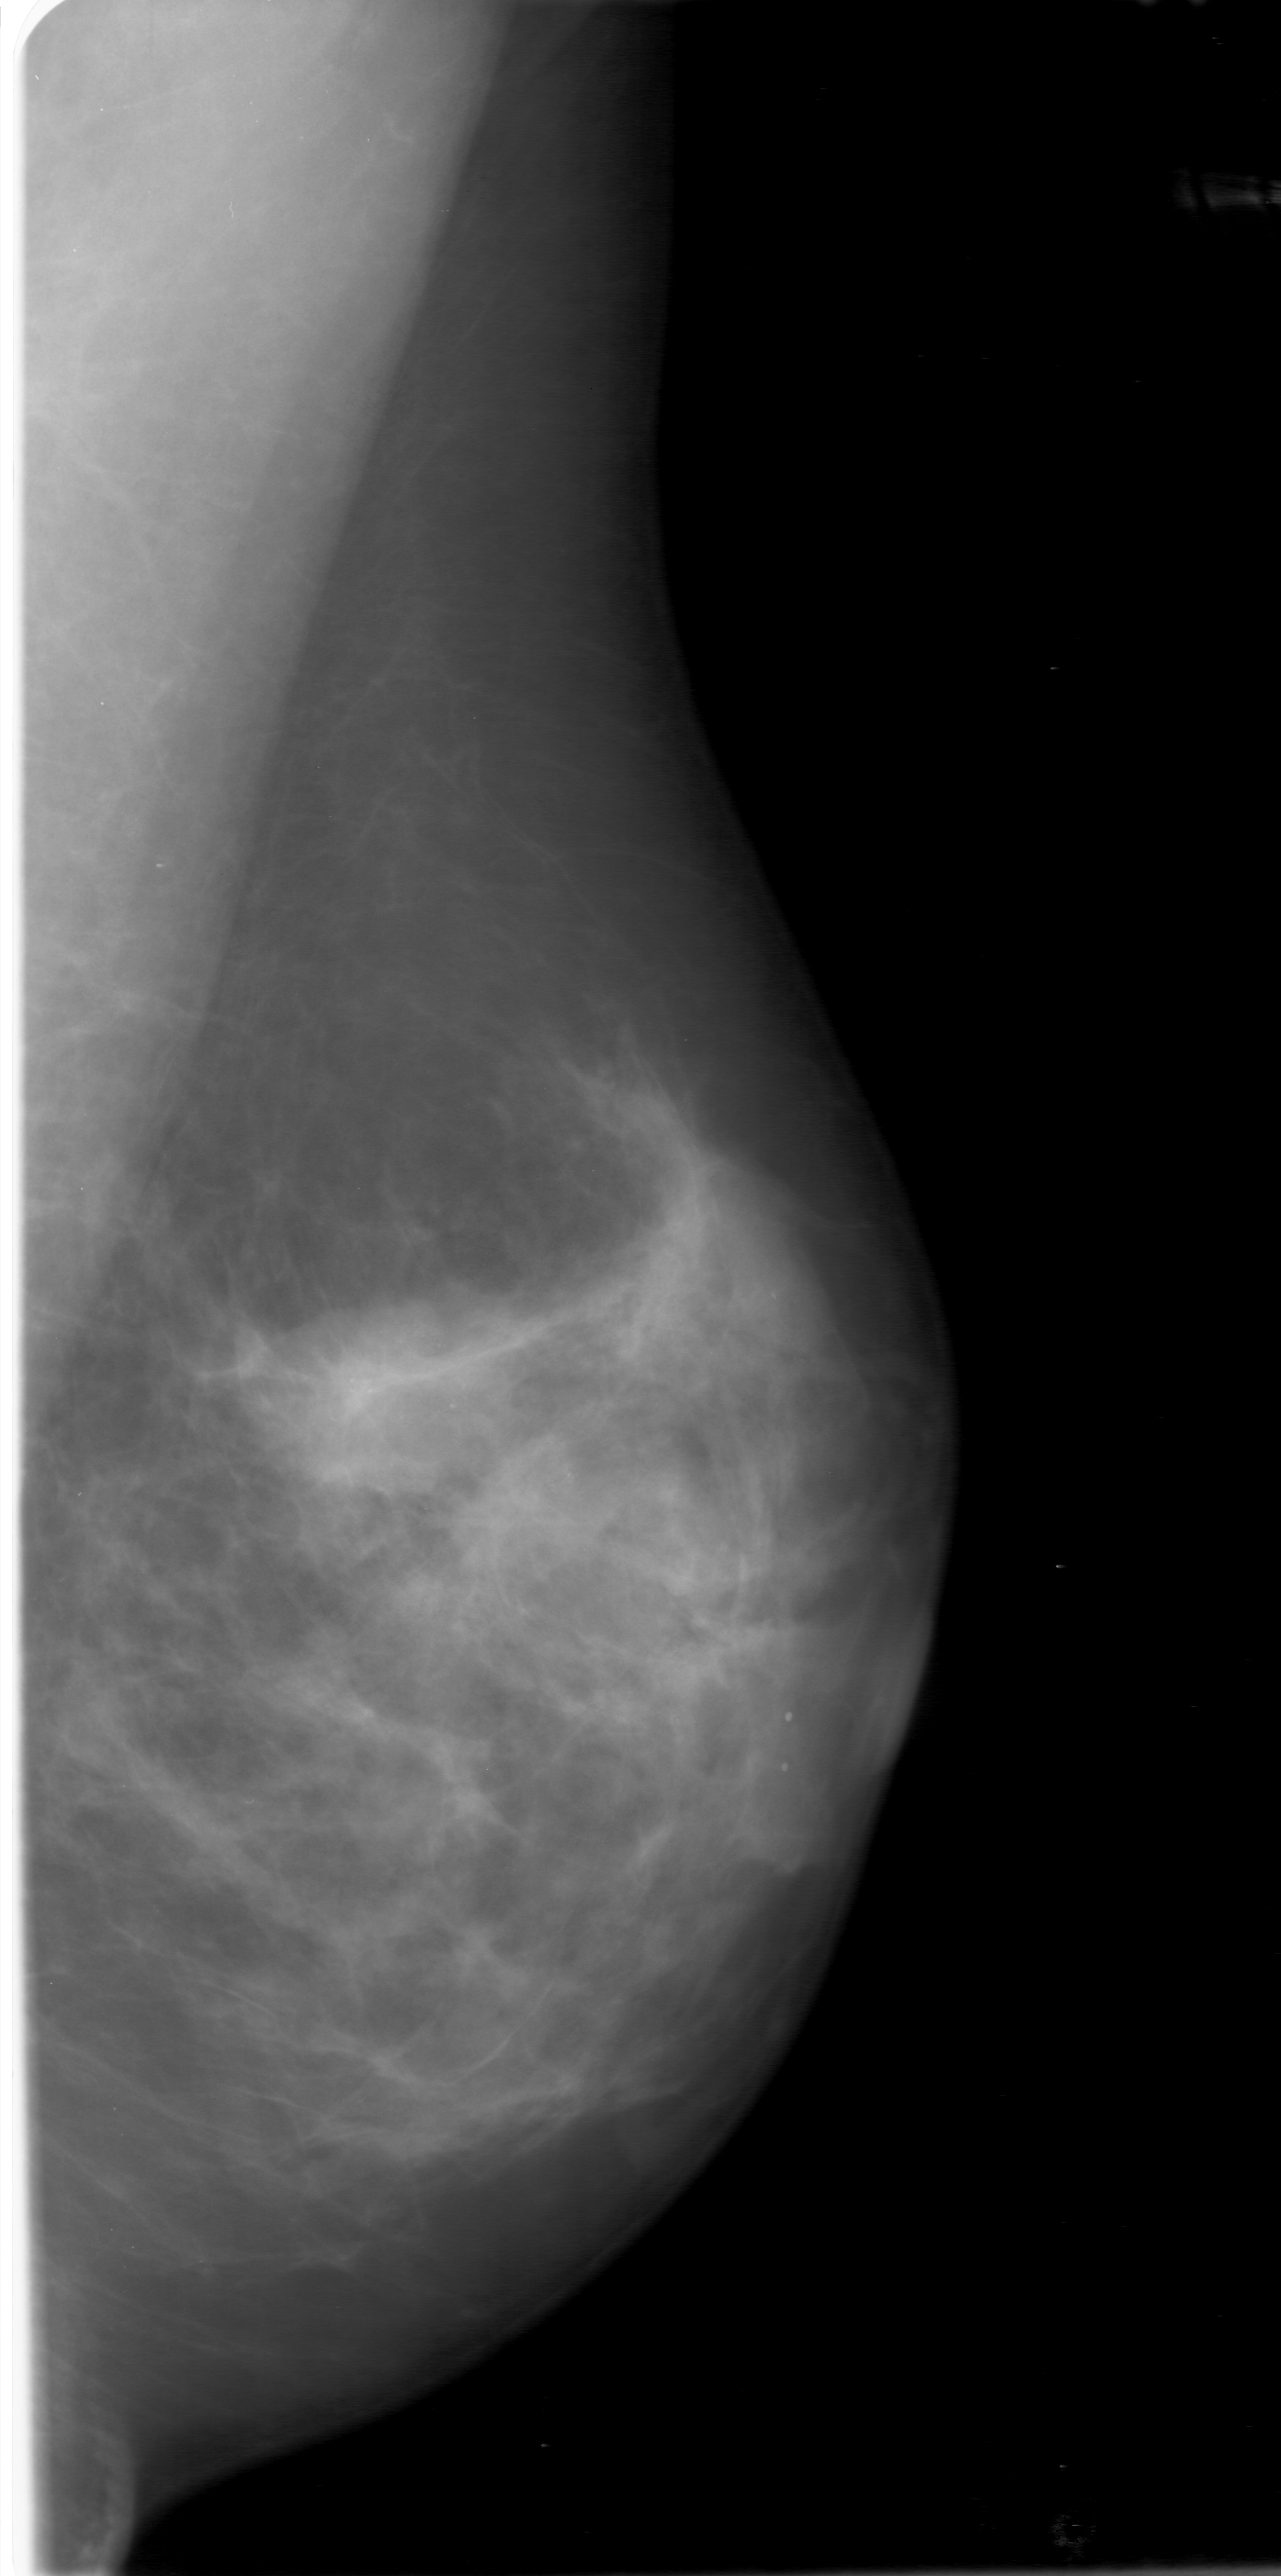
Scanned film-screen mammogram. Left breast. MLO view. Breast composition: scattered fibroglandular densities (BI-RADS density category 2 of 4). 1281 × 2576 image matrix.
Expert-marked regions of interest on this image (one box per marked abnormality):
- calcifications, morphology amorphous, distribution segmental; BI-RADS assessment category 4; pathology (as recorded): malignant: bounding box <202,1144,870,1679> (left, top, right, bottom; pixels)